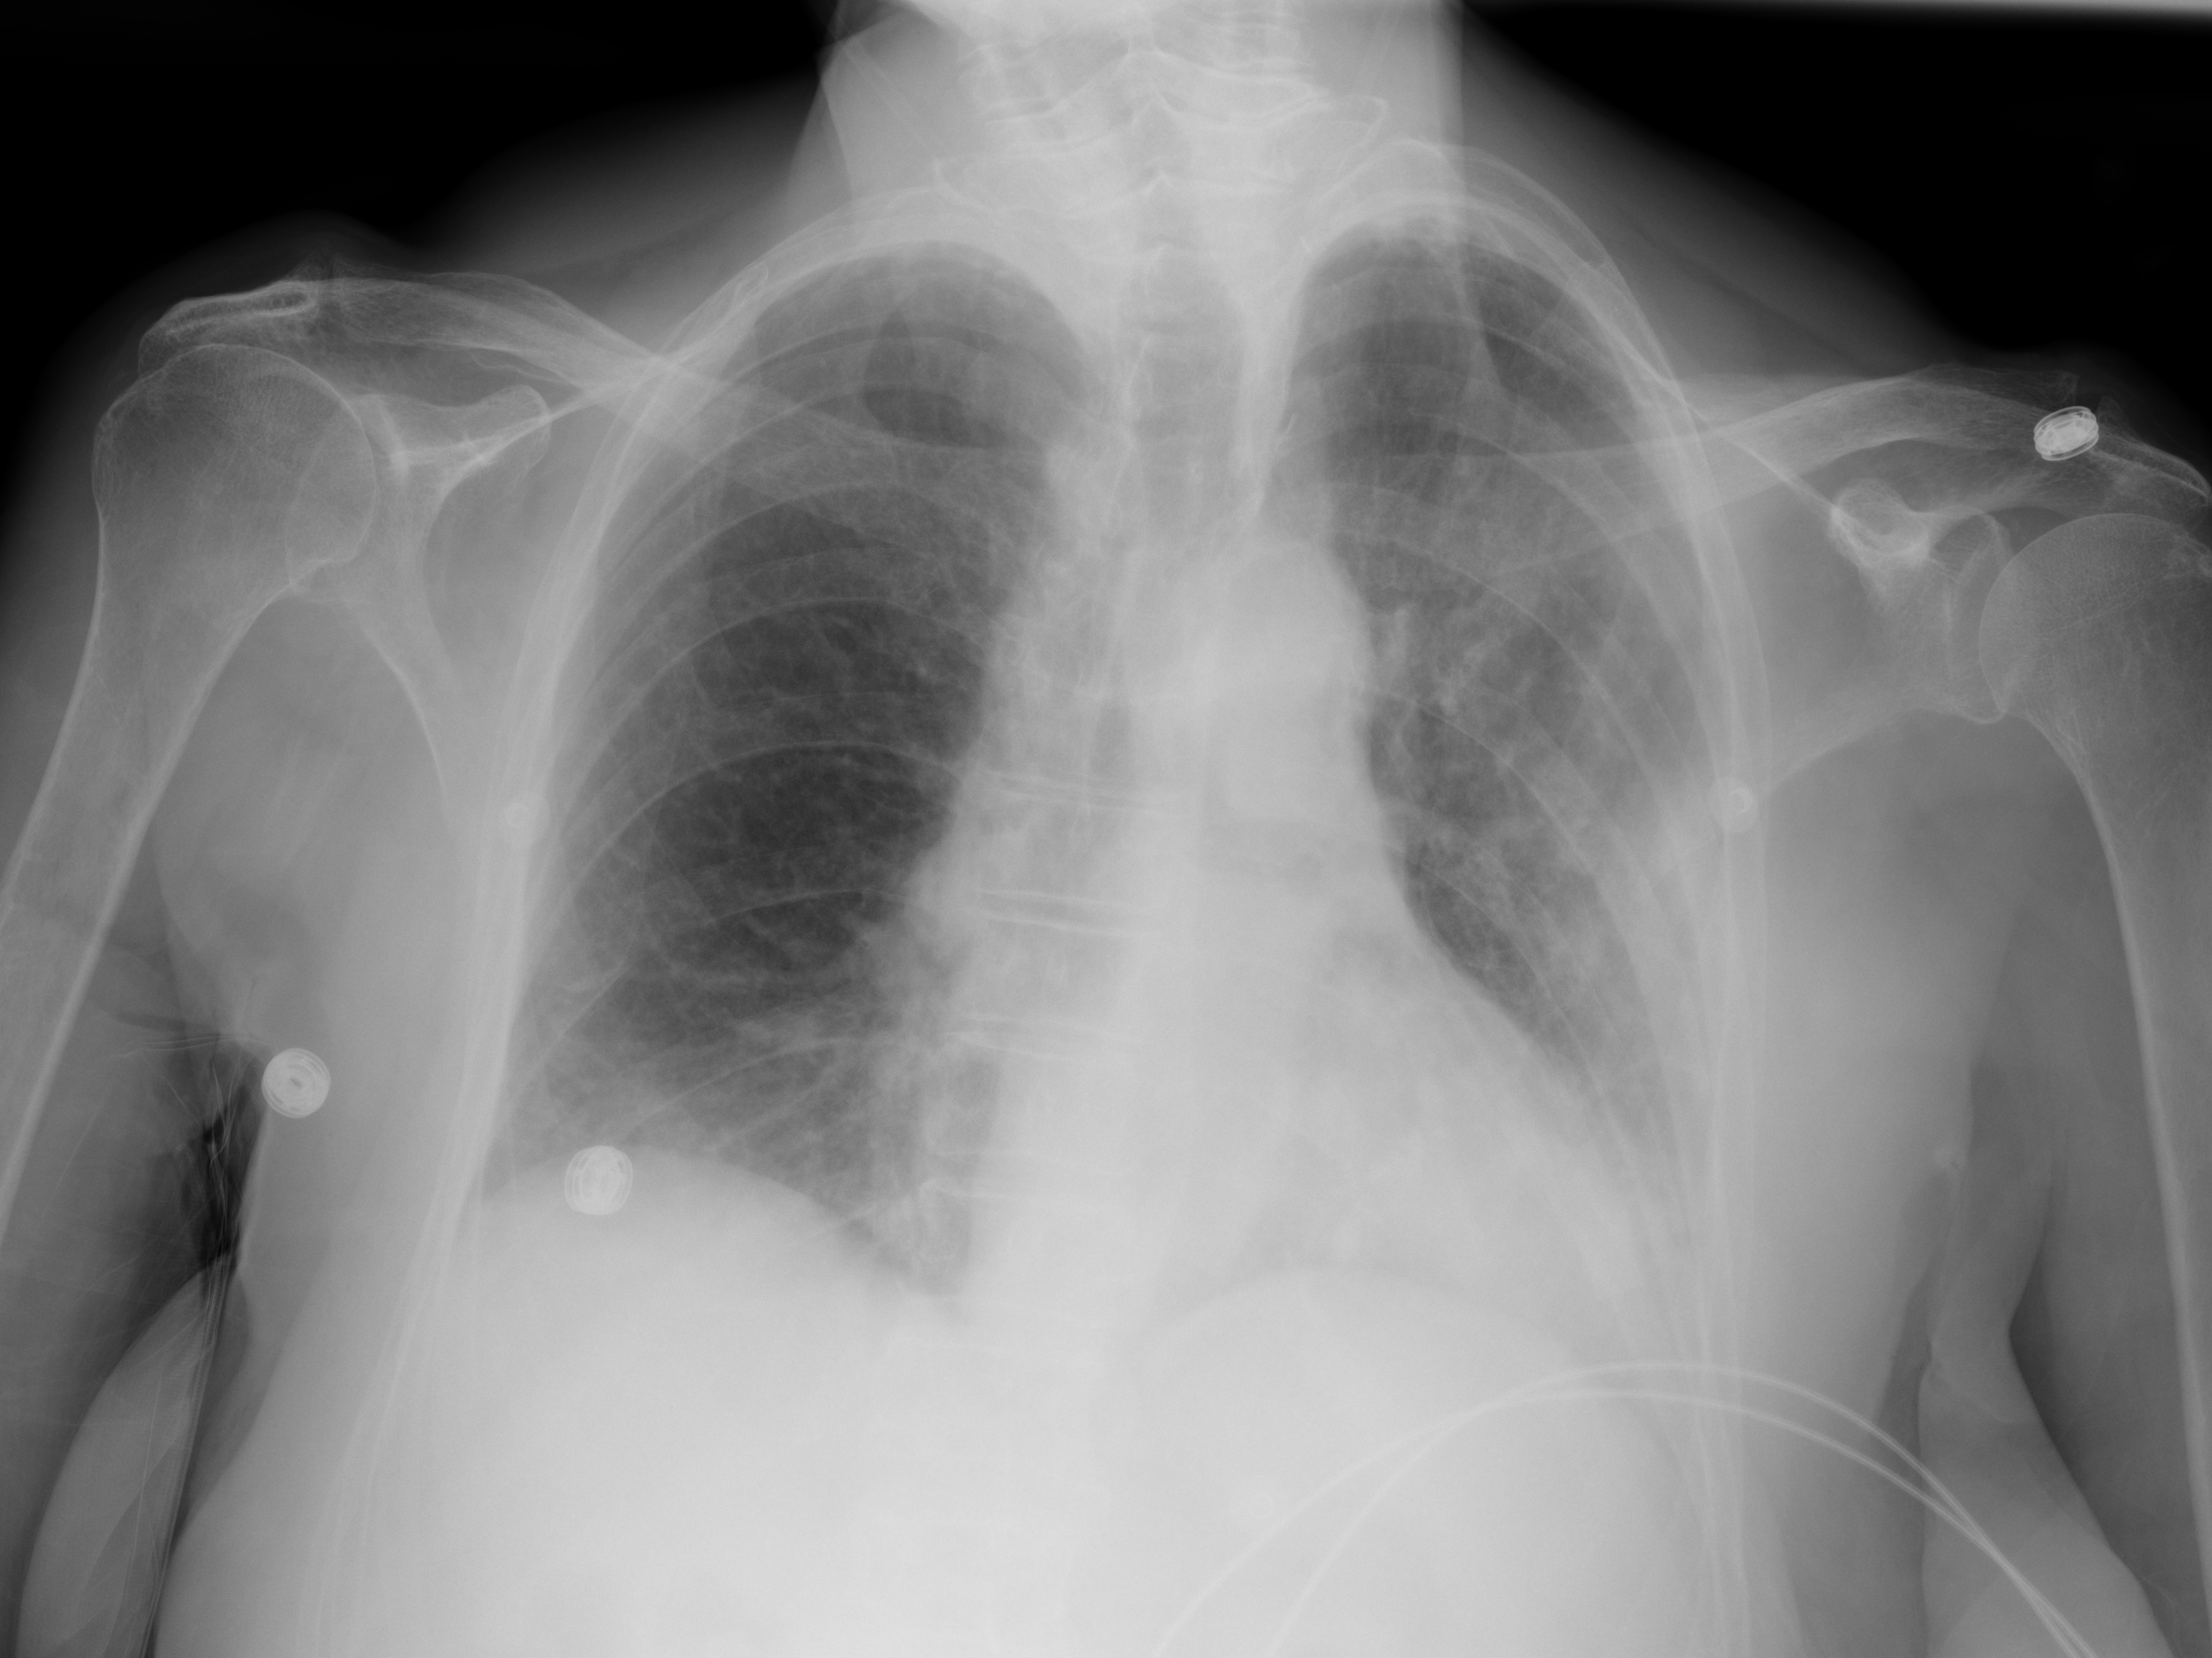
Portable chest radiograph, AP projection. Female patient, age 75 years; imaged 0 days after the COVID-19 diagnosis.
Radiologist key findings (as recorded): Patchy ground-glass opacities in the left lung and in the right lower lobe which may be infectious in etiology.